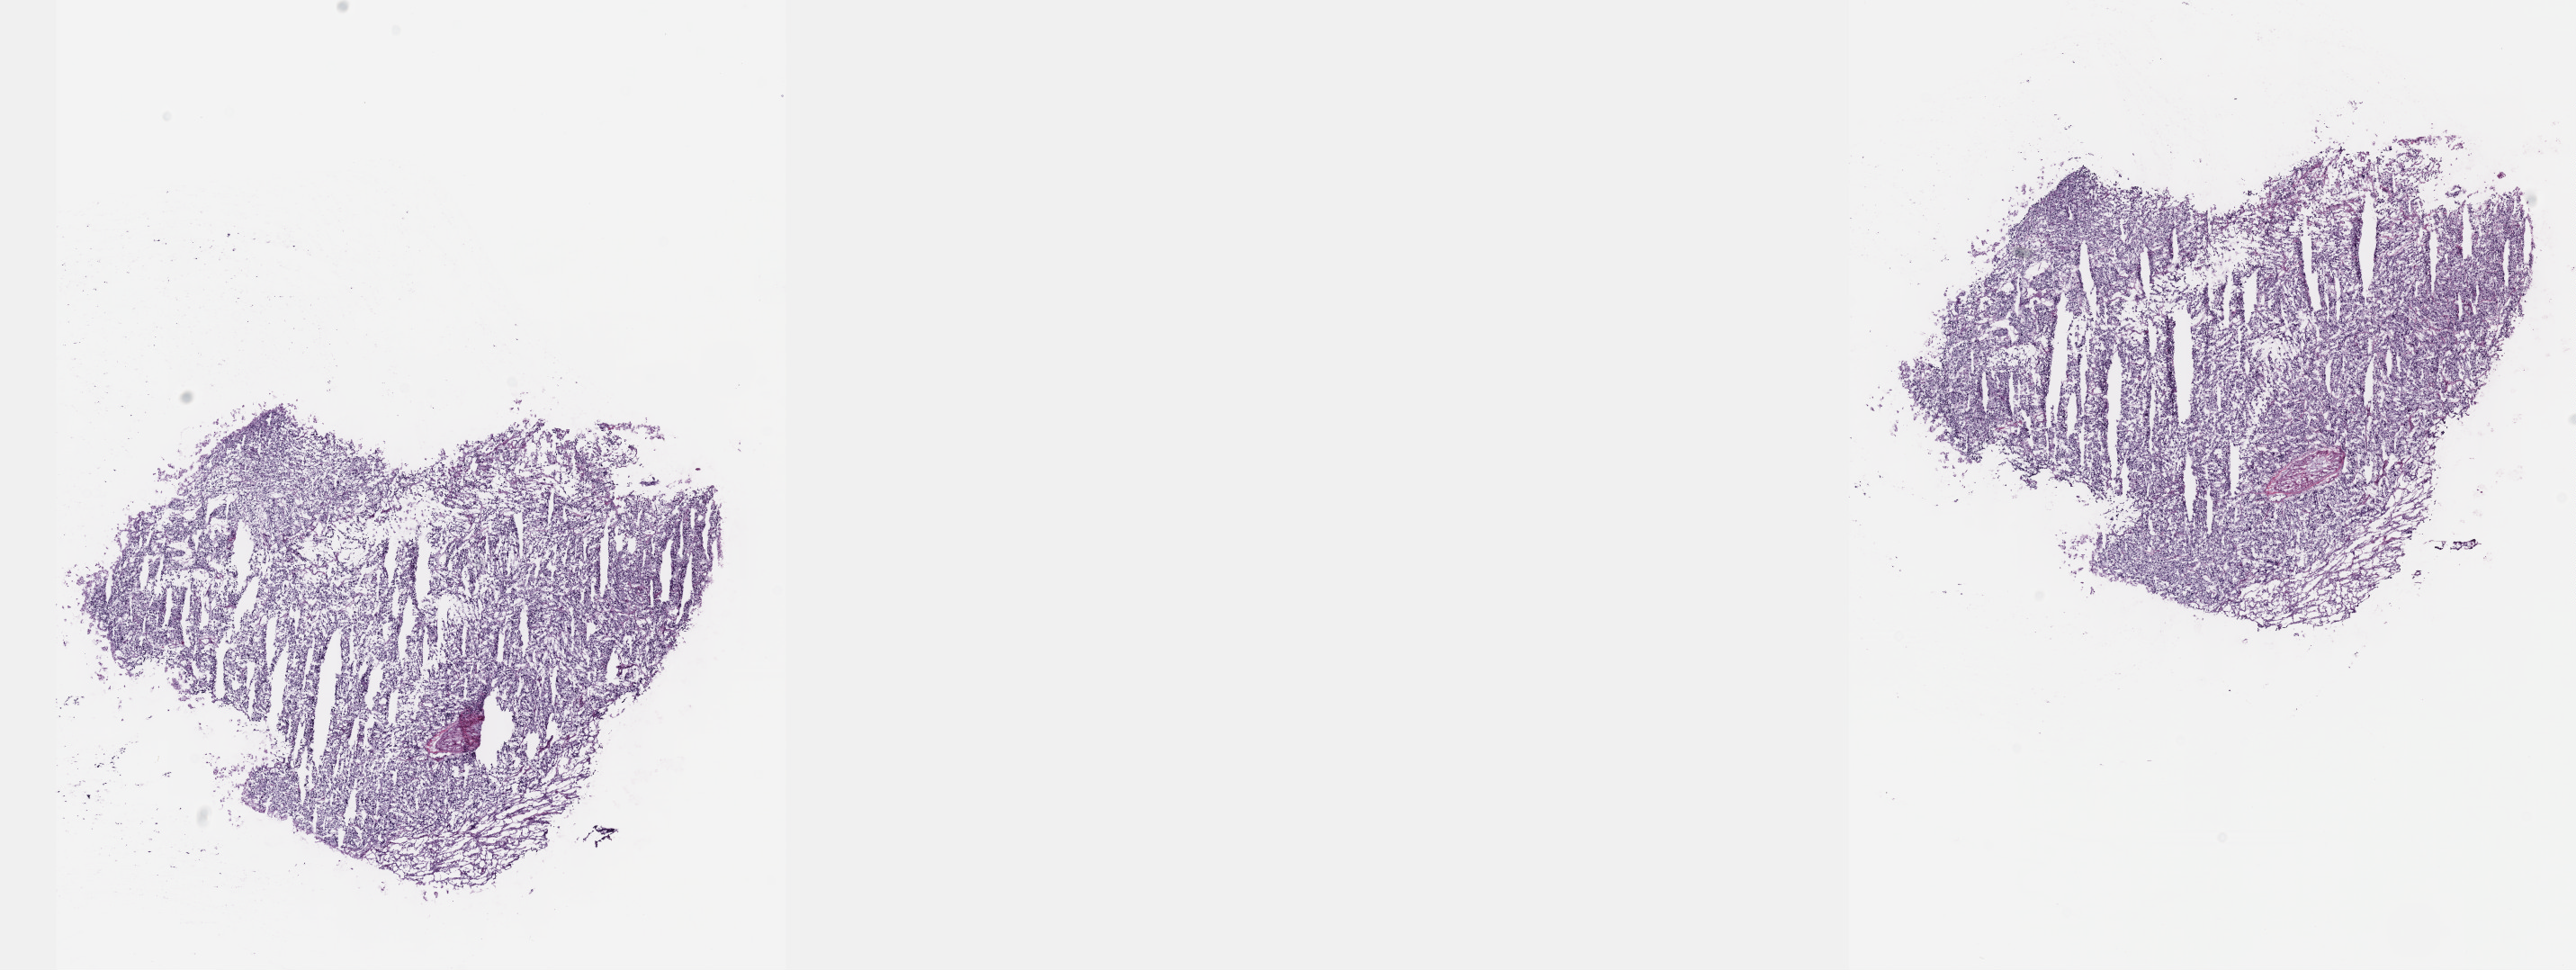
Digitized H&E-stained tissue section (whole slide) — a low-resolution overview of the entire scanned area, about 23.1 x 8.7 mm (from a 40x scan). Frozen section. Adrenal gland, primary tumour sample. Patient: male, age at initial diagnosis 54 years. Slide review estimates, as recorded: tumour cells 95%, tumour nuclei 95%, normal cells 0%, stromal cells 5%, necrosis 0%. Inflammatory infiltration, as recorded: lymphocyte infiltration 0%, monocyte infiltration 0%, neutrophil infiltration 0%.
Diagnosis: Pheochromocytoma, NOS. Laterality: left.